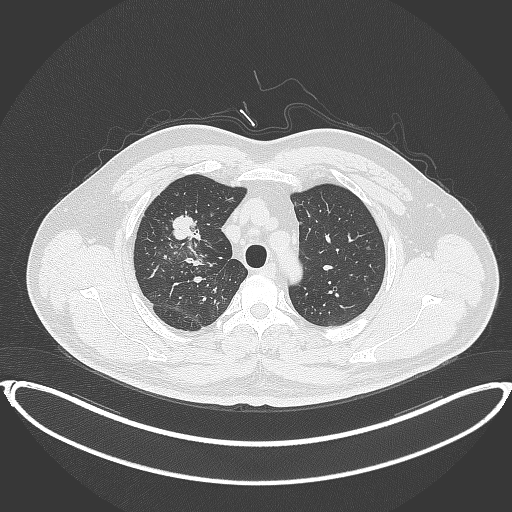
Chest CT, one axial slice. Slice 303 of 399 in the series (ordered by position). Reconstruction kernel B70f. 120 kVp. Lung window (W 1500 / L -600 HU). 512 × 512 image matrix. Patient: male, 53 years. From the clinical record (not read from this slice): clinical TNM (as recorded): T2a N0 M0.
Structures marked on this image (rectangle marked by the reading radiologist):
- lung tumour (recorded histology: adenocarcinoma): bounding box (x1, y1, x2, y2) in pixels: (169, 211, 202, 244)